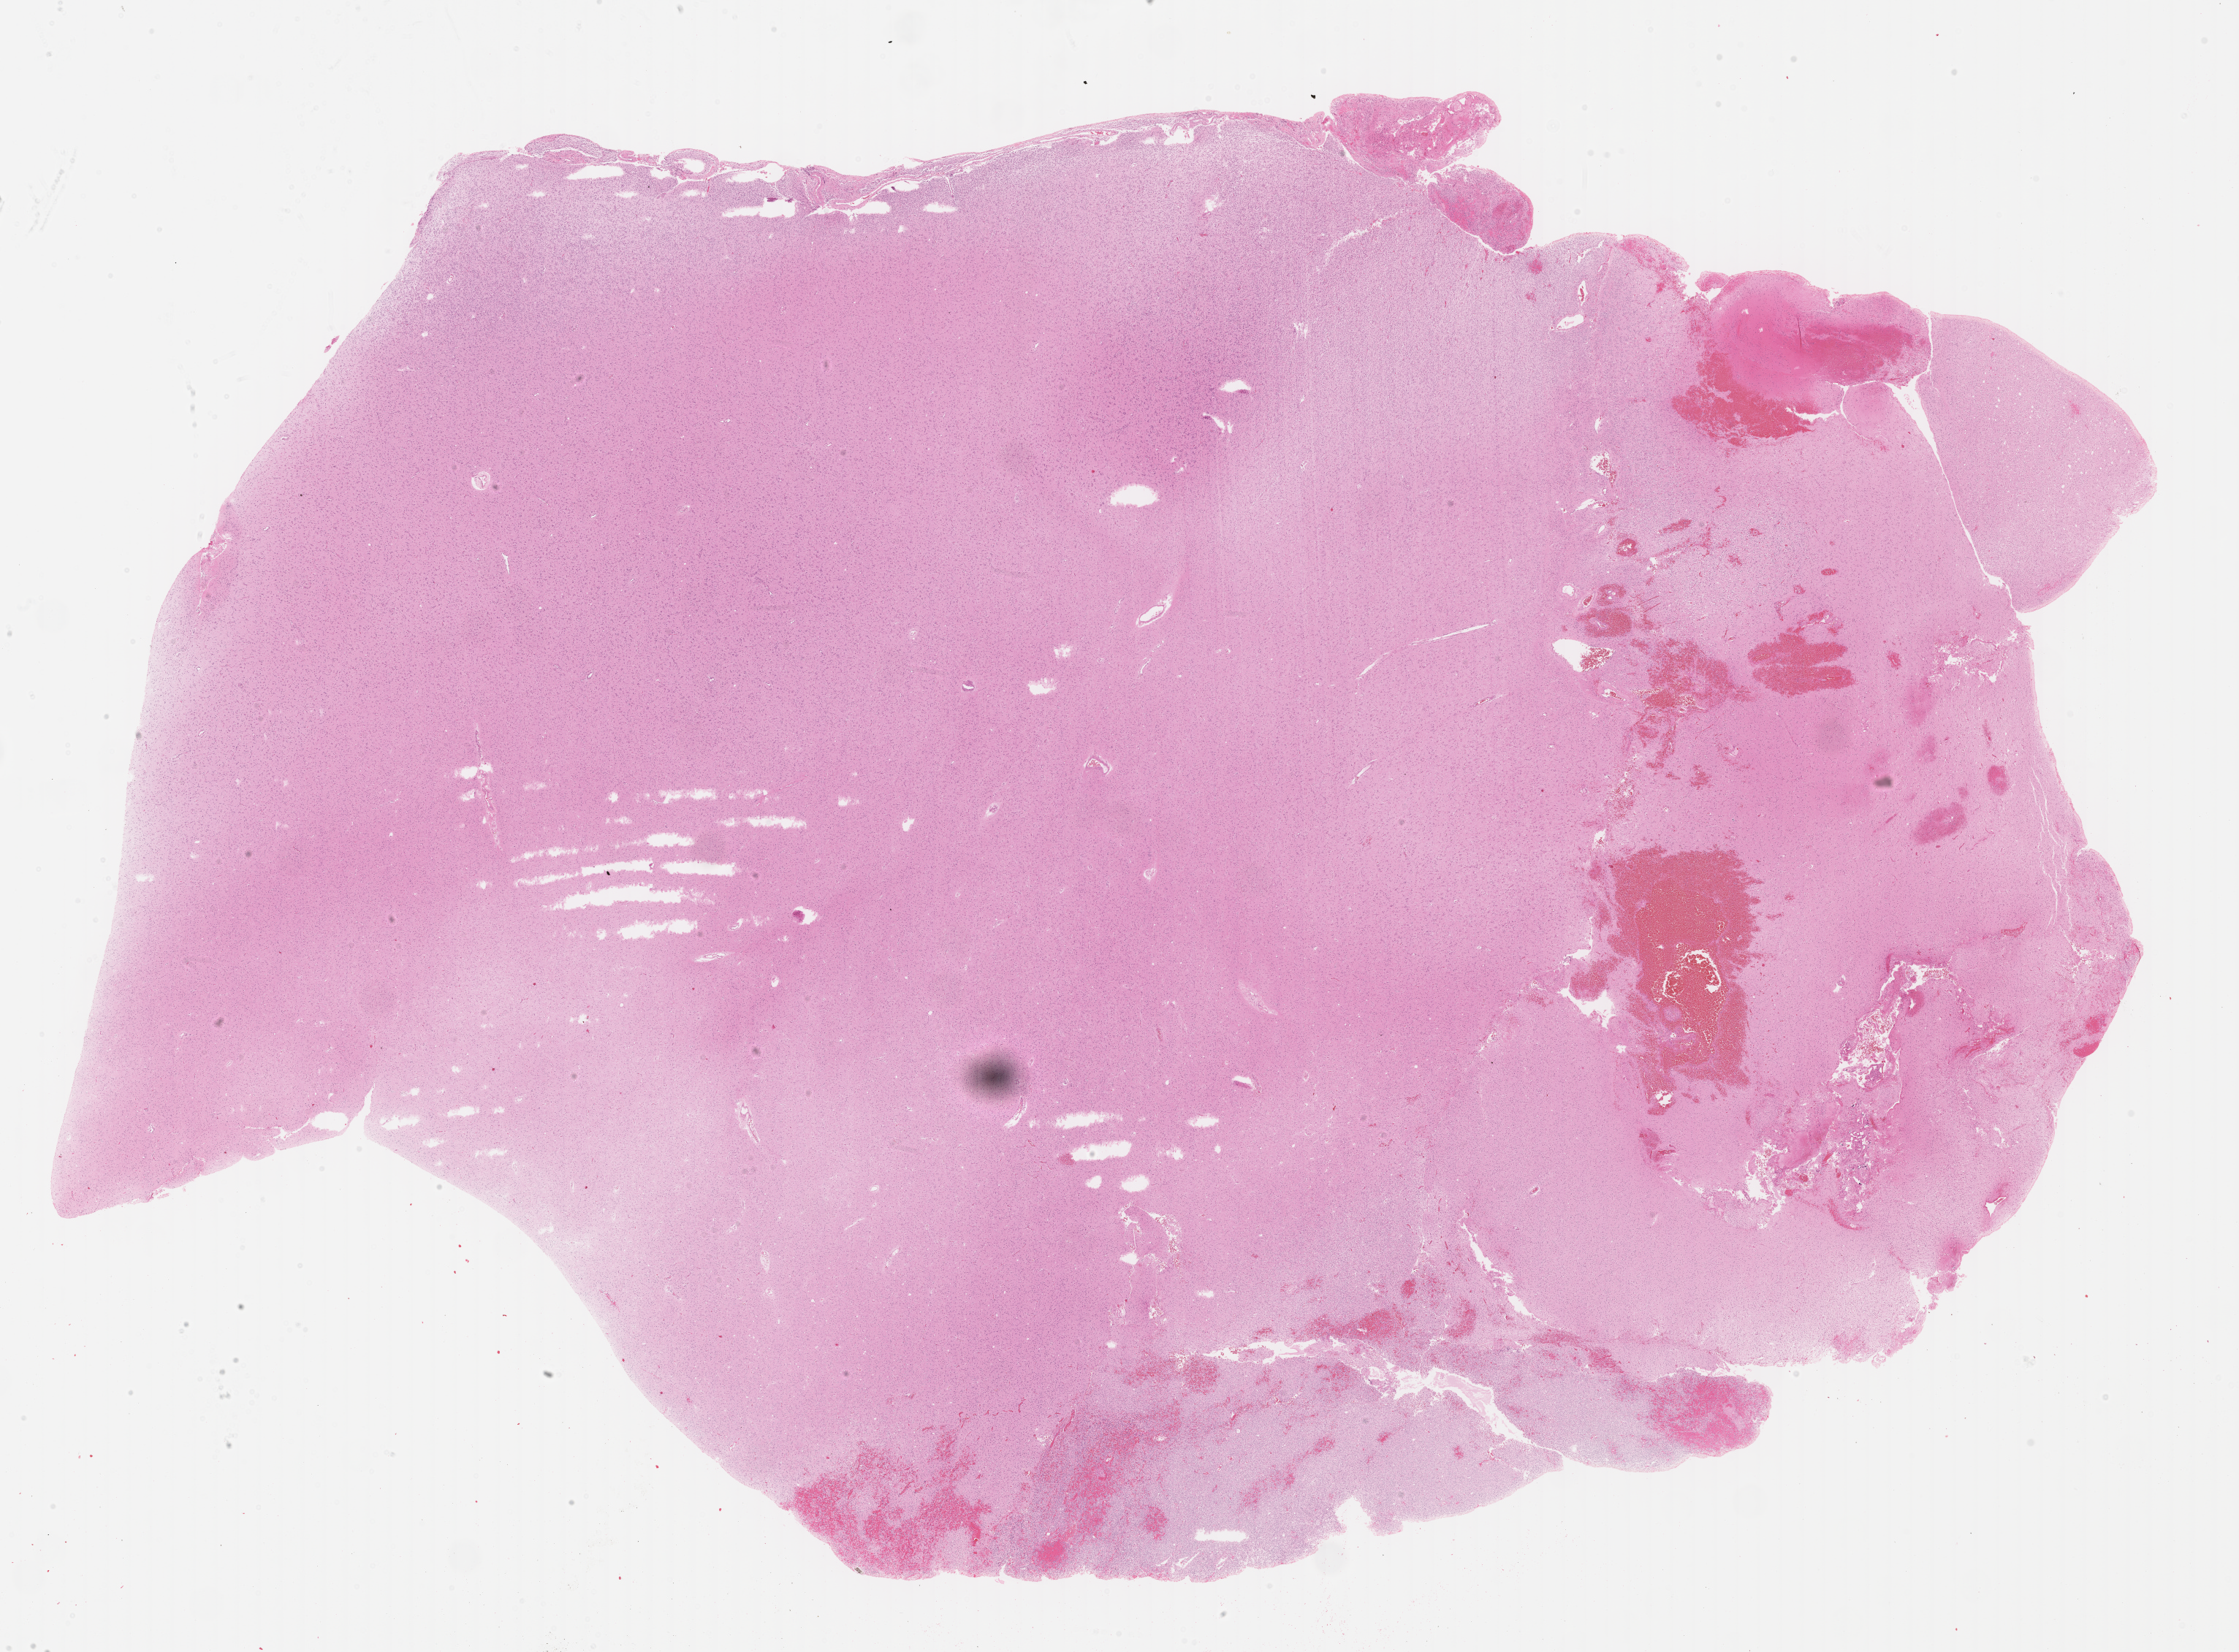
Hematoxylin and eosin (H&E) stained whole-slide image, low-resolution overview of the scanned area, about 24.7 x 18.2 mm. Formalin-fixed paraffin-embedded (FFPE) diagnostic section. Sample: primary tumour, brain. Male patient; age at initial diagnosis 40 years. Histologic grade: G2 (moderately differentiated).
Histologic diagnosis: Oligodendroglioma, NOS (cerebrum).